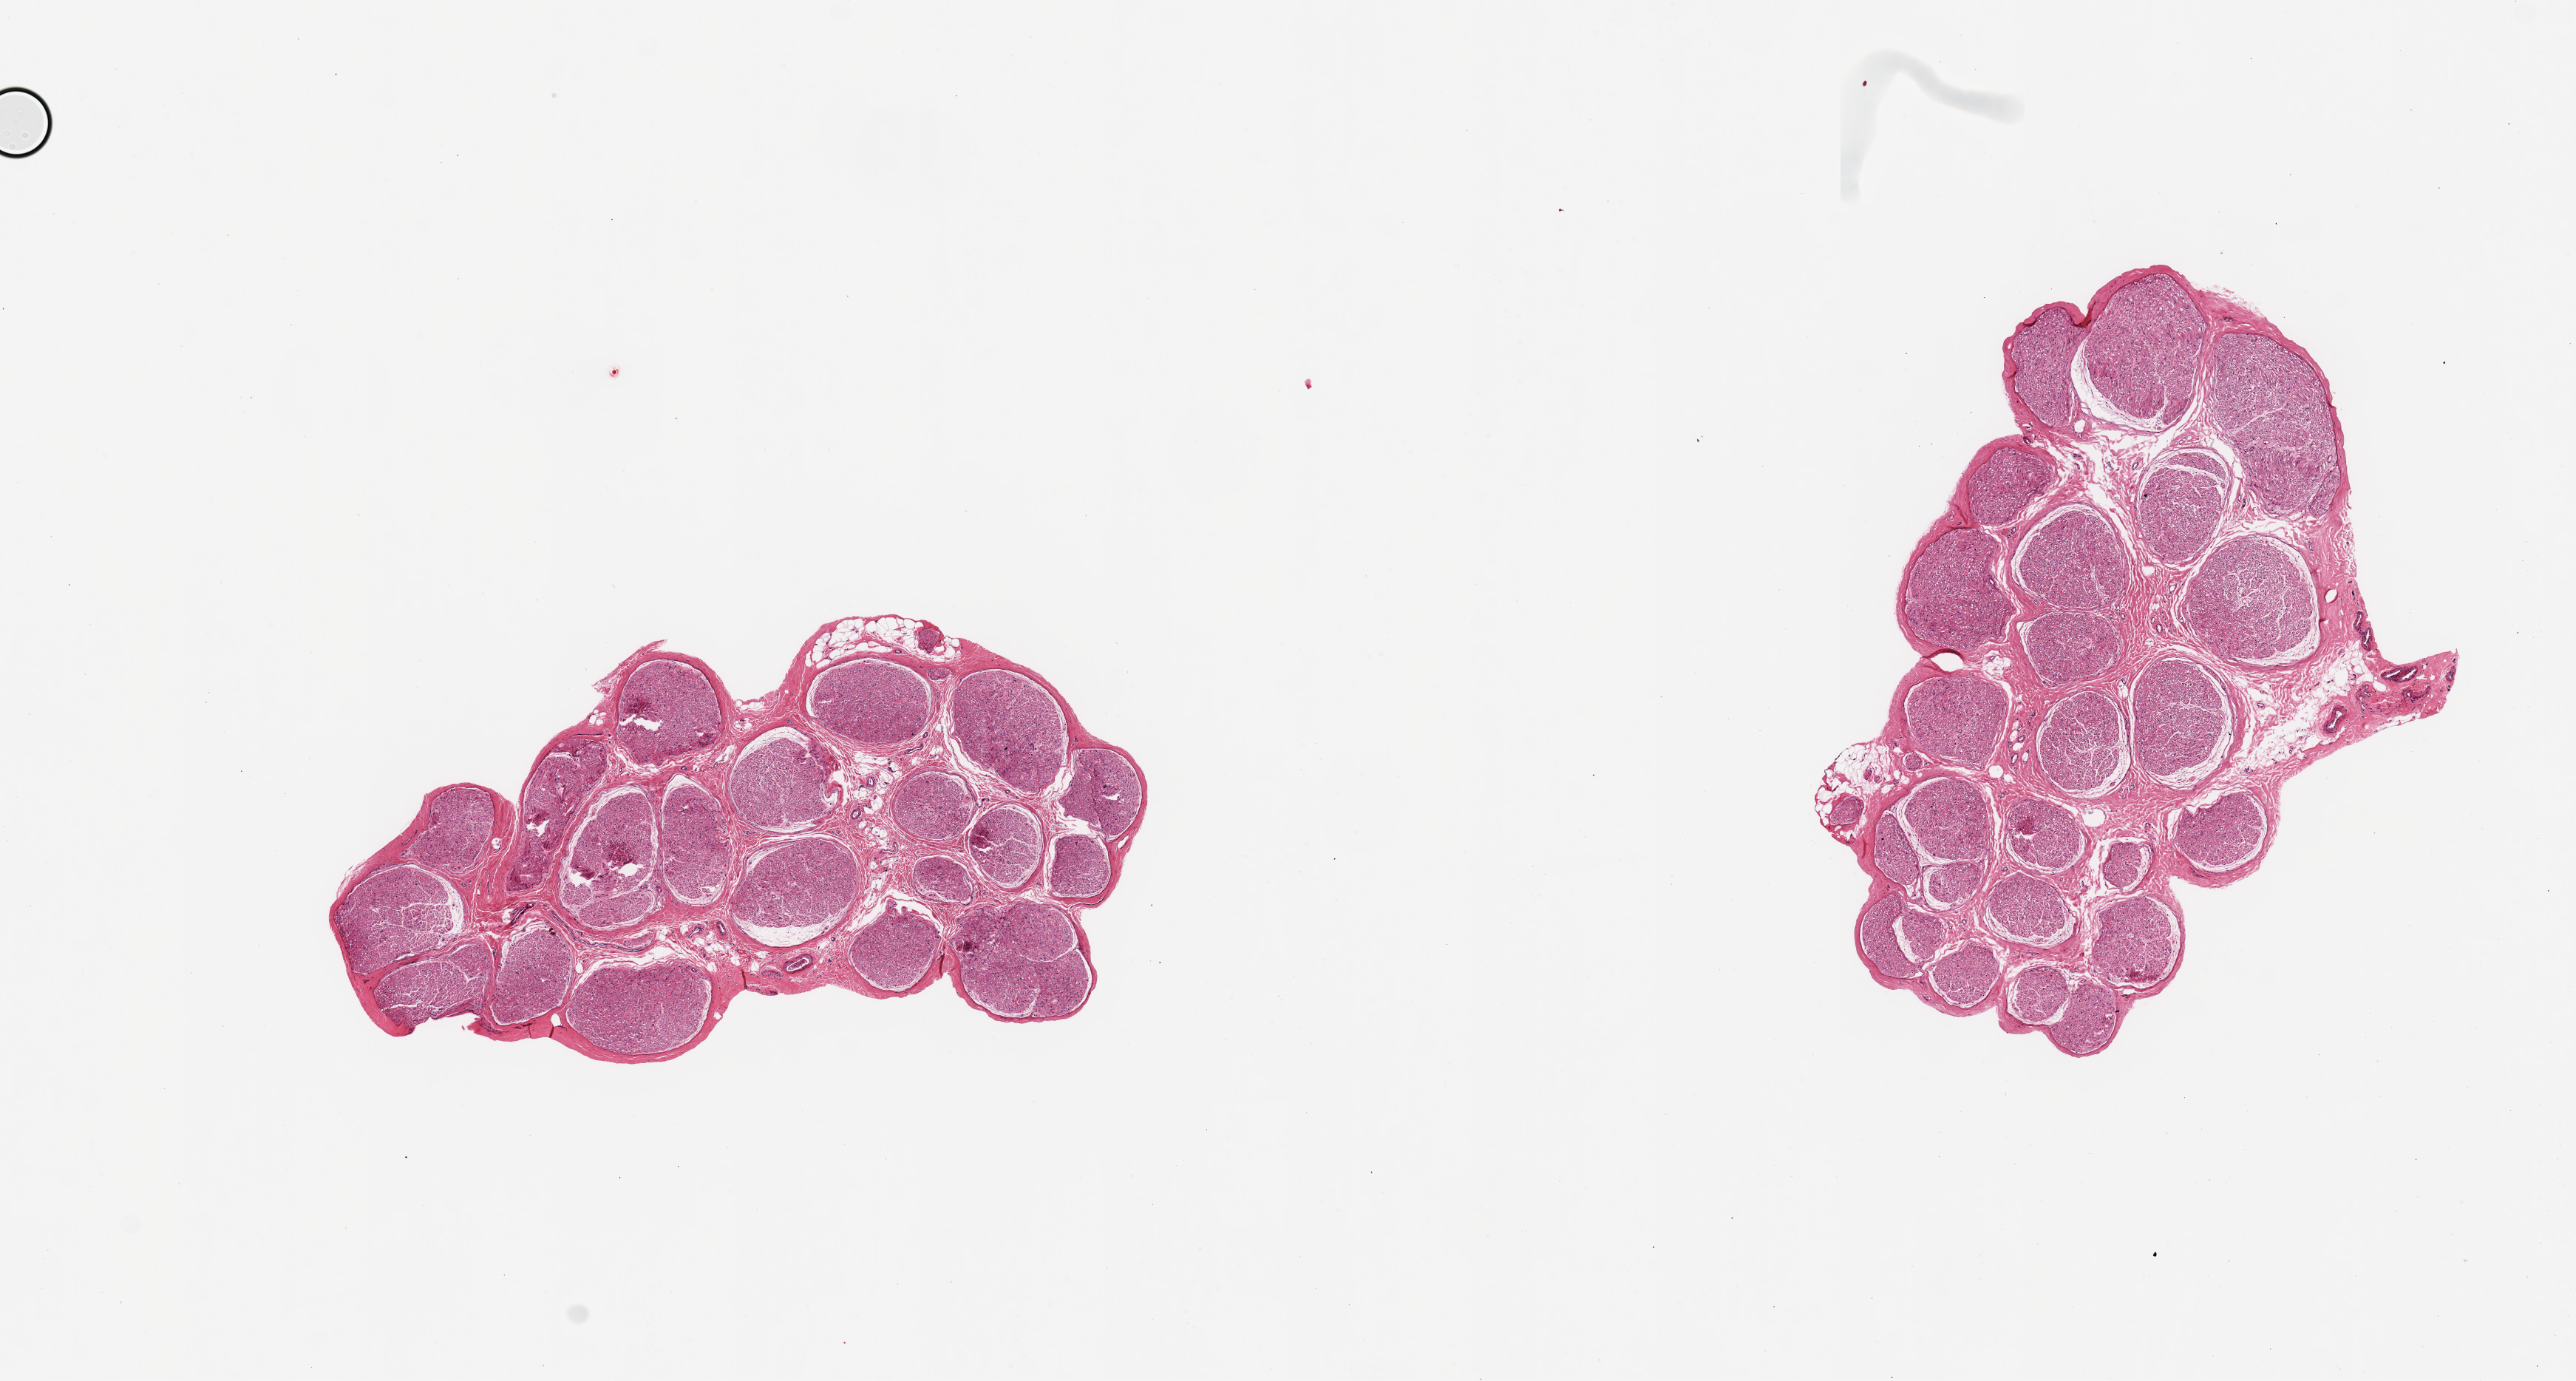
Digitized H&E-stained section, shown as a low-resolution overview of the whole scanned area (about 13.8 x 7.4 mm, acquisition: 20x scan), PAXgene-fixed, paraffin-embedded tissue, target tissue: tibial nerve, tissue donor sample. Donor sex: female.
Reviewer comment on this tissue sample: 2 pieces, 4x3 & 4x3mm; well trimmed nerves.